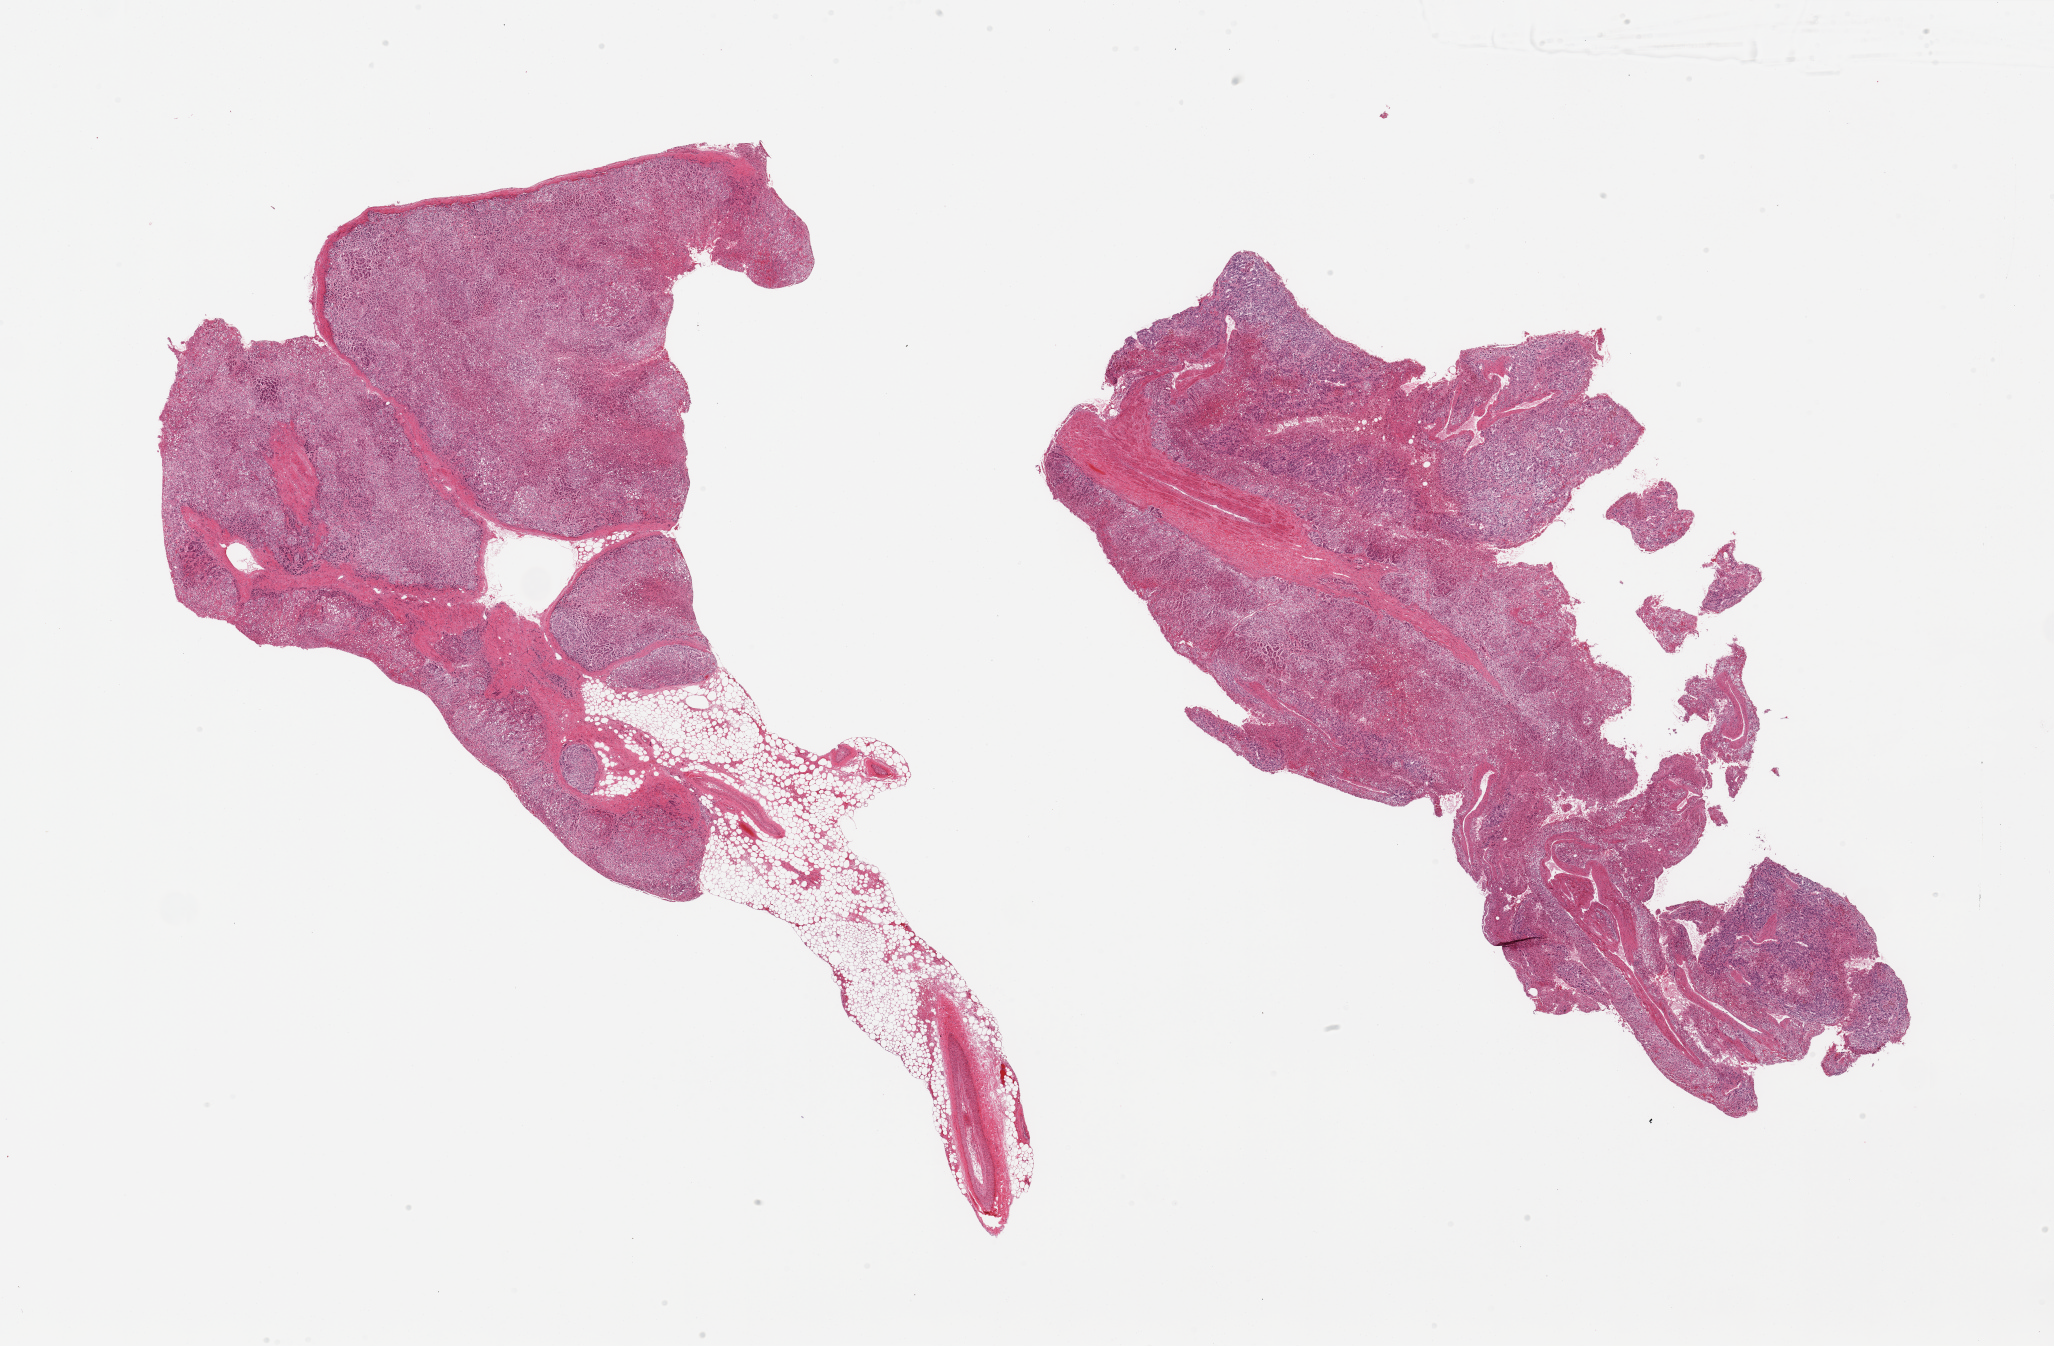
Digitized haematoxylin and eosin-stained section, shown as a low-resolution overview of the whole scanned area (about 32.5 x 21.3 mm), PAXgene-fixed paraffin-embedded (PFPE) section, section of adrenal gland (target tissue), tissue donor sample. Male donor.
• pathologist's review note for this sample: 2 pieces; cortex only with ~10% adherent fat to one piece